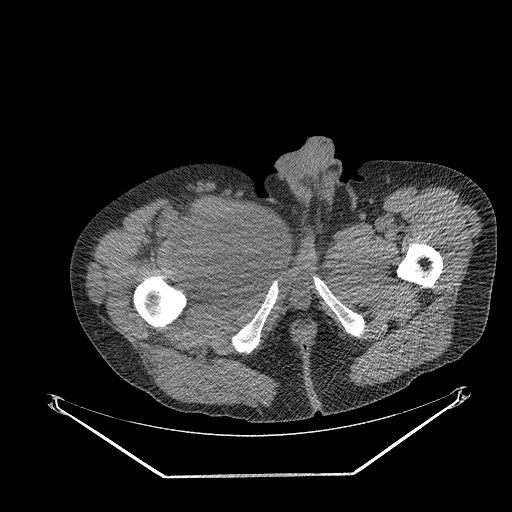
CT of an extremity soft-tissue mass (from a PET/CT study), one axial slice; slice 285 of 311 in the series (ordered by position); reconstruction kernel STANDARD; soft-tissue window (W 400 / L 40 HU); 3.75 mm slice thickness; 512 × 512 image matrix, field of view 500 × 500 mm. Male patient. From the clinical record (not read from this slice): histological type: undifferentiated - pleiomorphic; grade: high; site of the primary tumour: right thigh.
Annotated regions visible in this slice (expert contour drawn on MRI and transferred to this co-registered scan by the dataset authors):
- gross tumour volume including surrounding oedema: bounding box [x1, y1, x2, y2] px = [192, 201, 259, 273]
- gross tumour volume (mass): [192, 206, 255, 266]